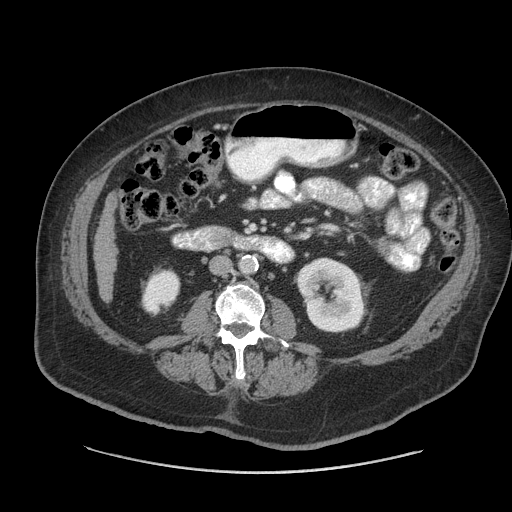
Contrast-enhanced abdominal CT (liver protocol), one axial slice. Position 12 of 91 along the scan axis. Reconstruction kernel STANDARD. 140 kVp. Soft-tissue window (W 400 / L 40 HU). 2.5 mm slice thickness. 512 × 512 image matrix, field of view 420 × 420 mm. Case-level facts recorded for this patient, not image findings: diagnosis: hepatocellular carcinoma (patient treated with transarterial chemoembolisation; whether this scan precedes or follows treatment is not stated here); TNM stage (as recorded): Stage-I; Child-Pugh class: A; tumour differentiation: well differentiated; tumour nodularity: uninodular.
Annotated regions visible in this slice (semi-automatic segmentation, software-assisted and operator-edited):
- liver parenchyma outside the tumour (the mass and vessels are separate outlines, so this box may not span the whole liver): bounding box [x1, y1, x2, y2] px = [94, 202, 118, 300]